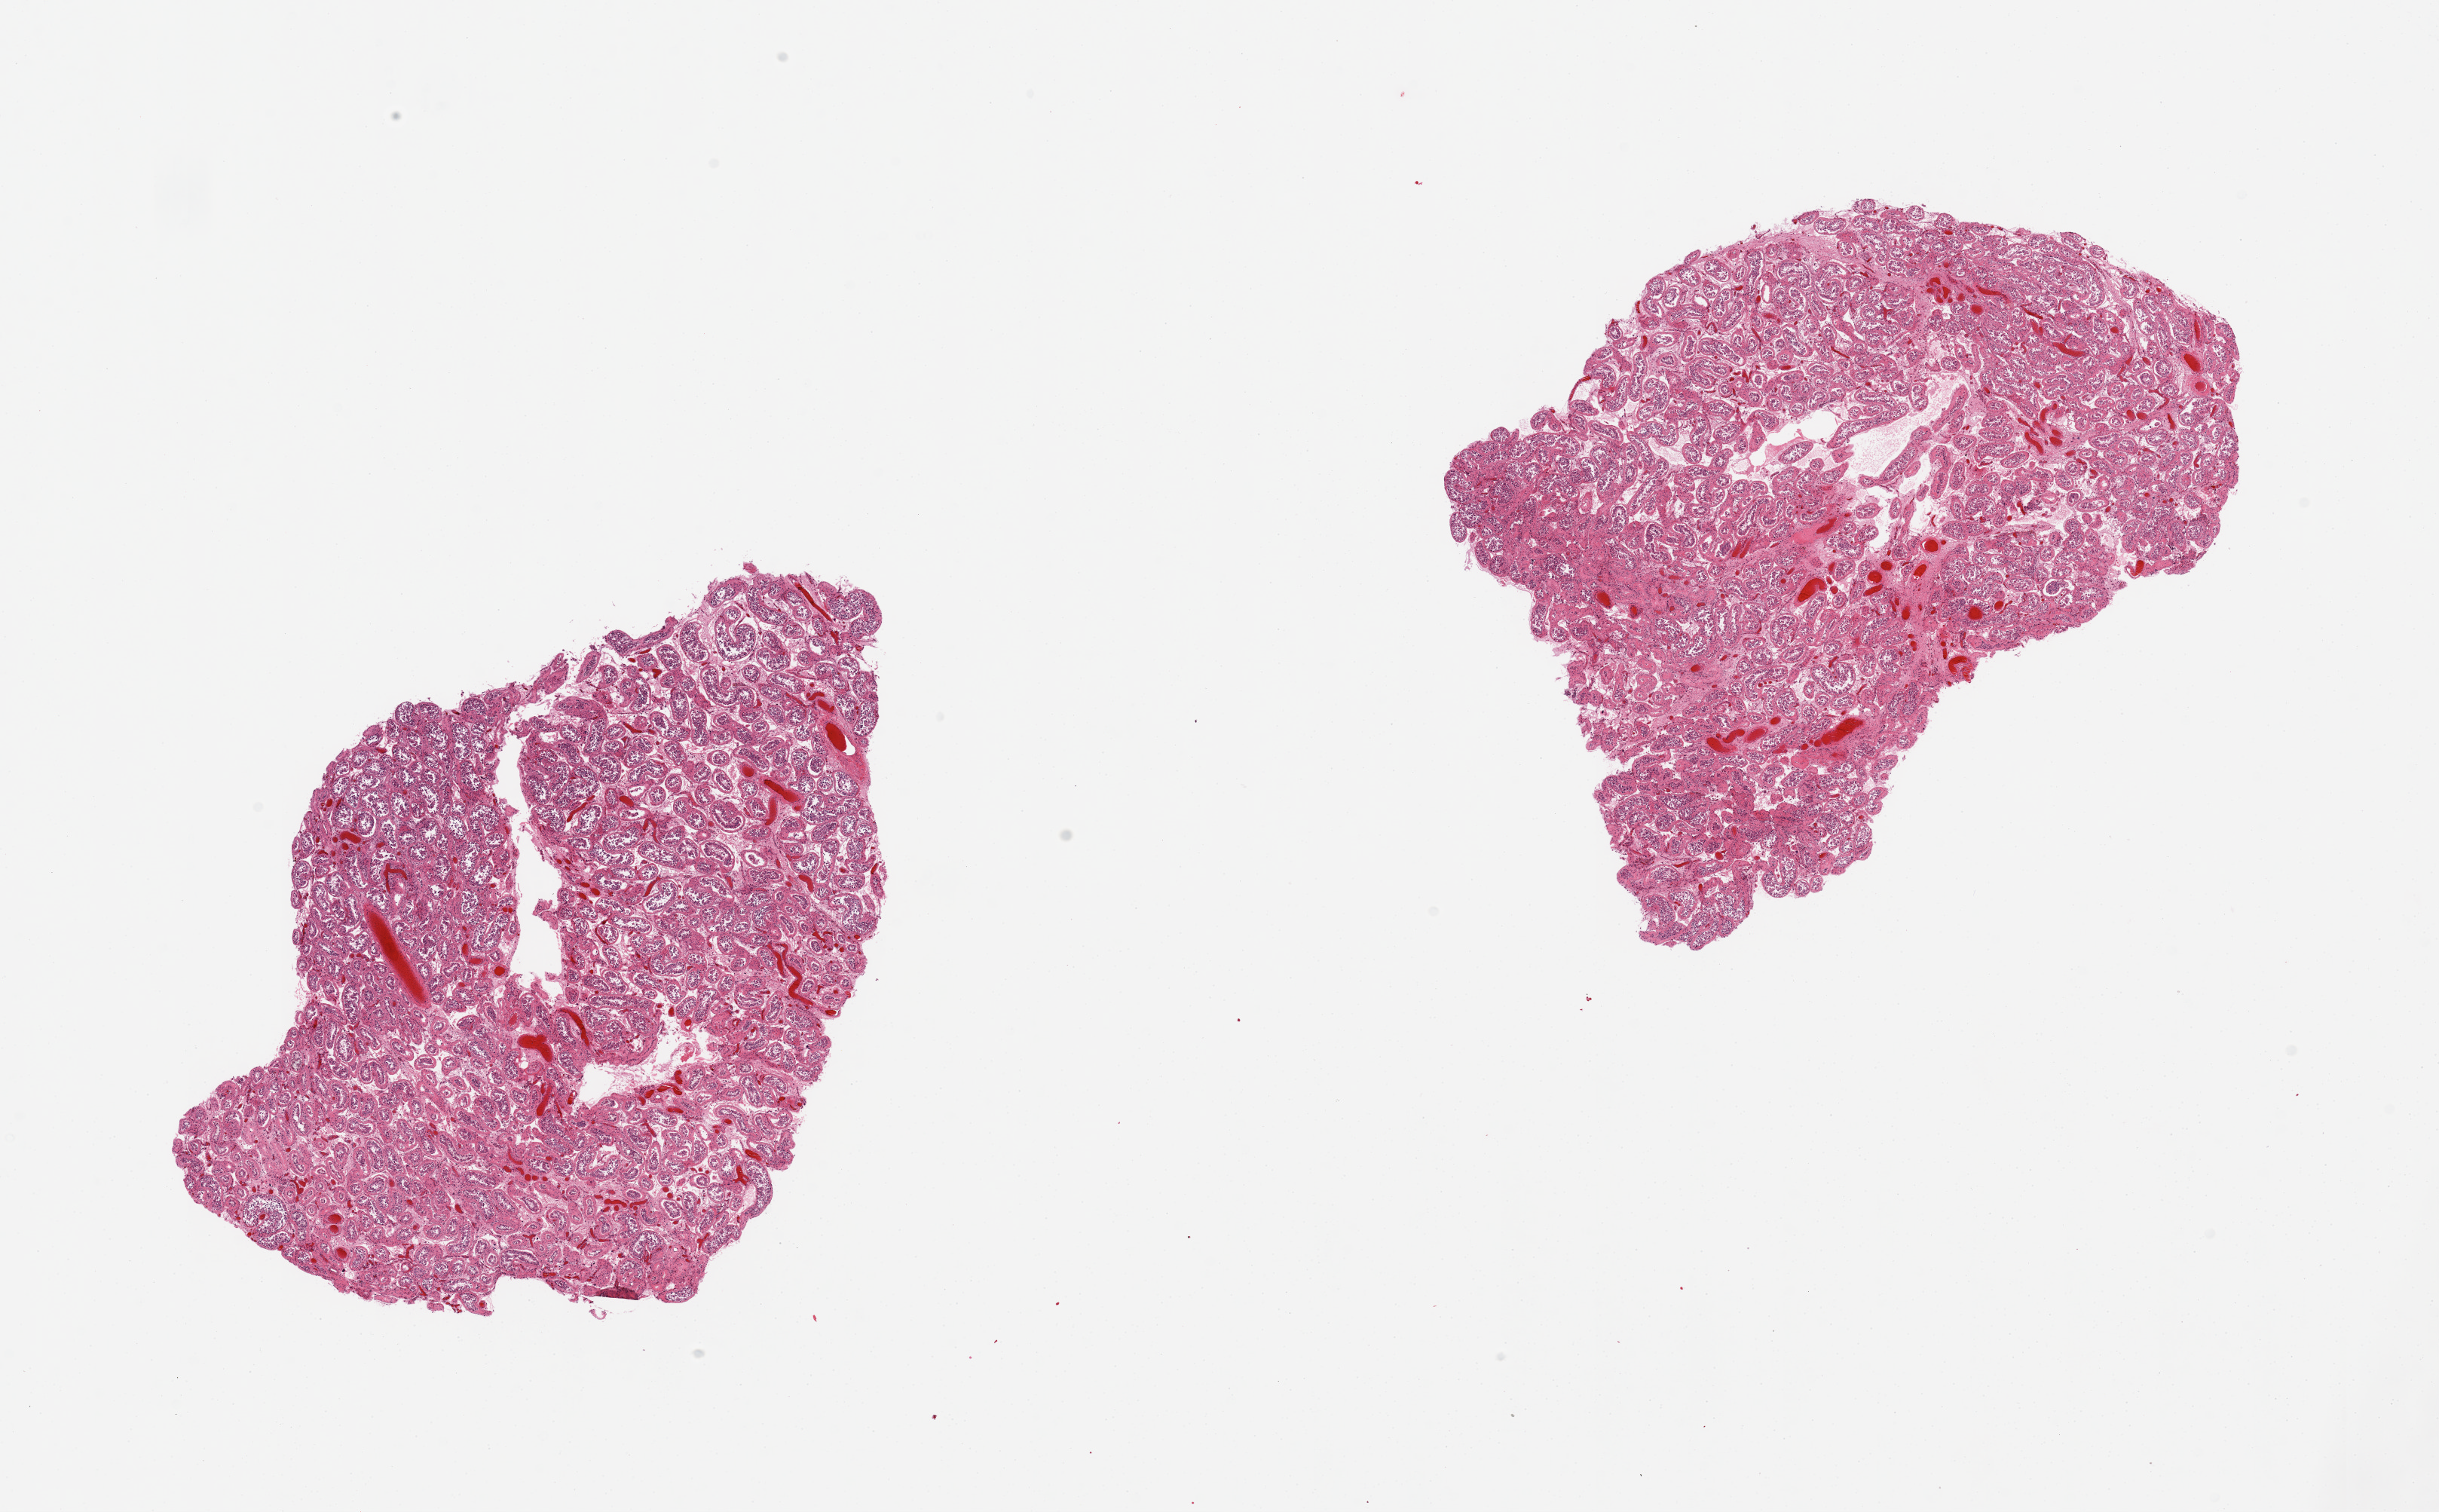
Haematoxylin and eosin whole-slide image, a low-resolution overview of the entire scanned area, about 25.6 x 15.9 mm, PAXgene-fixed, paraffin-embedded tissue, sampled site (target tissue): testis, tissue donor sample.
* reviewer comment on this tissue sample: 2 pieces spermatogenesis appears reduced; but marked autolysis precludes assessment